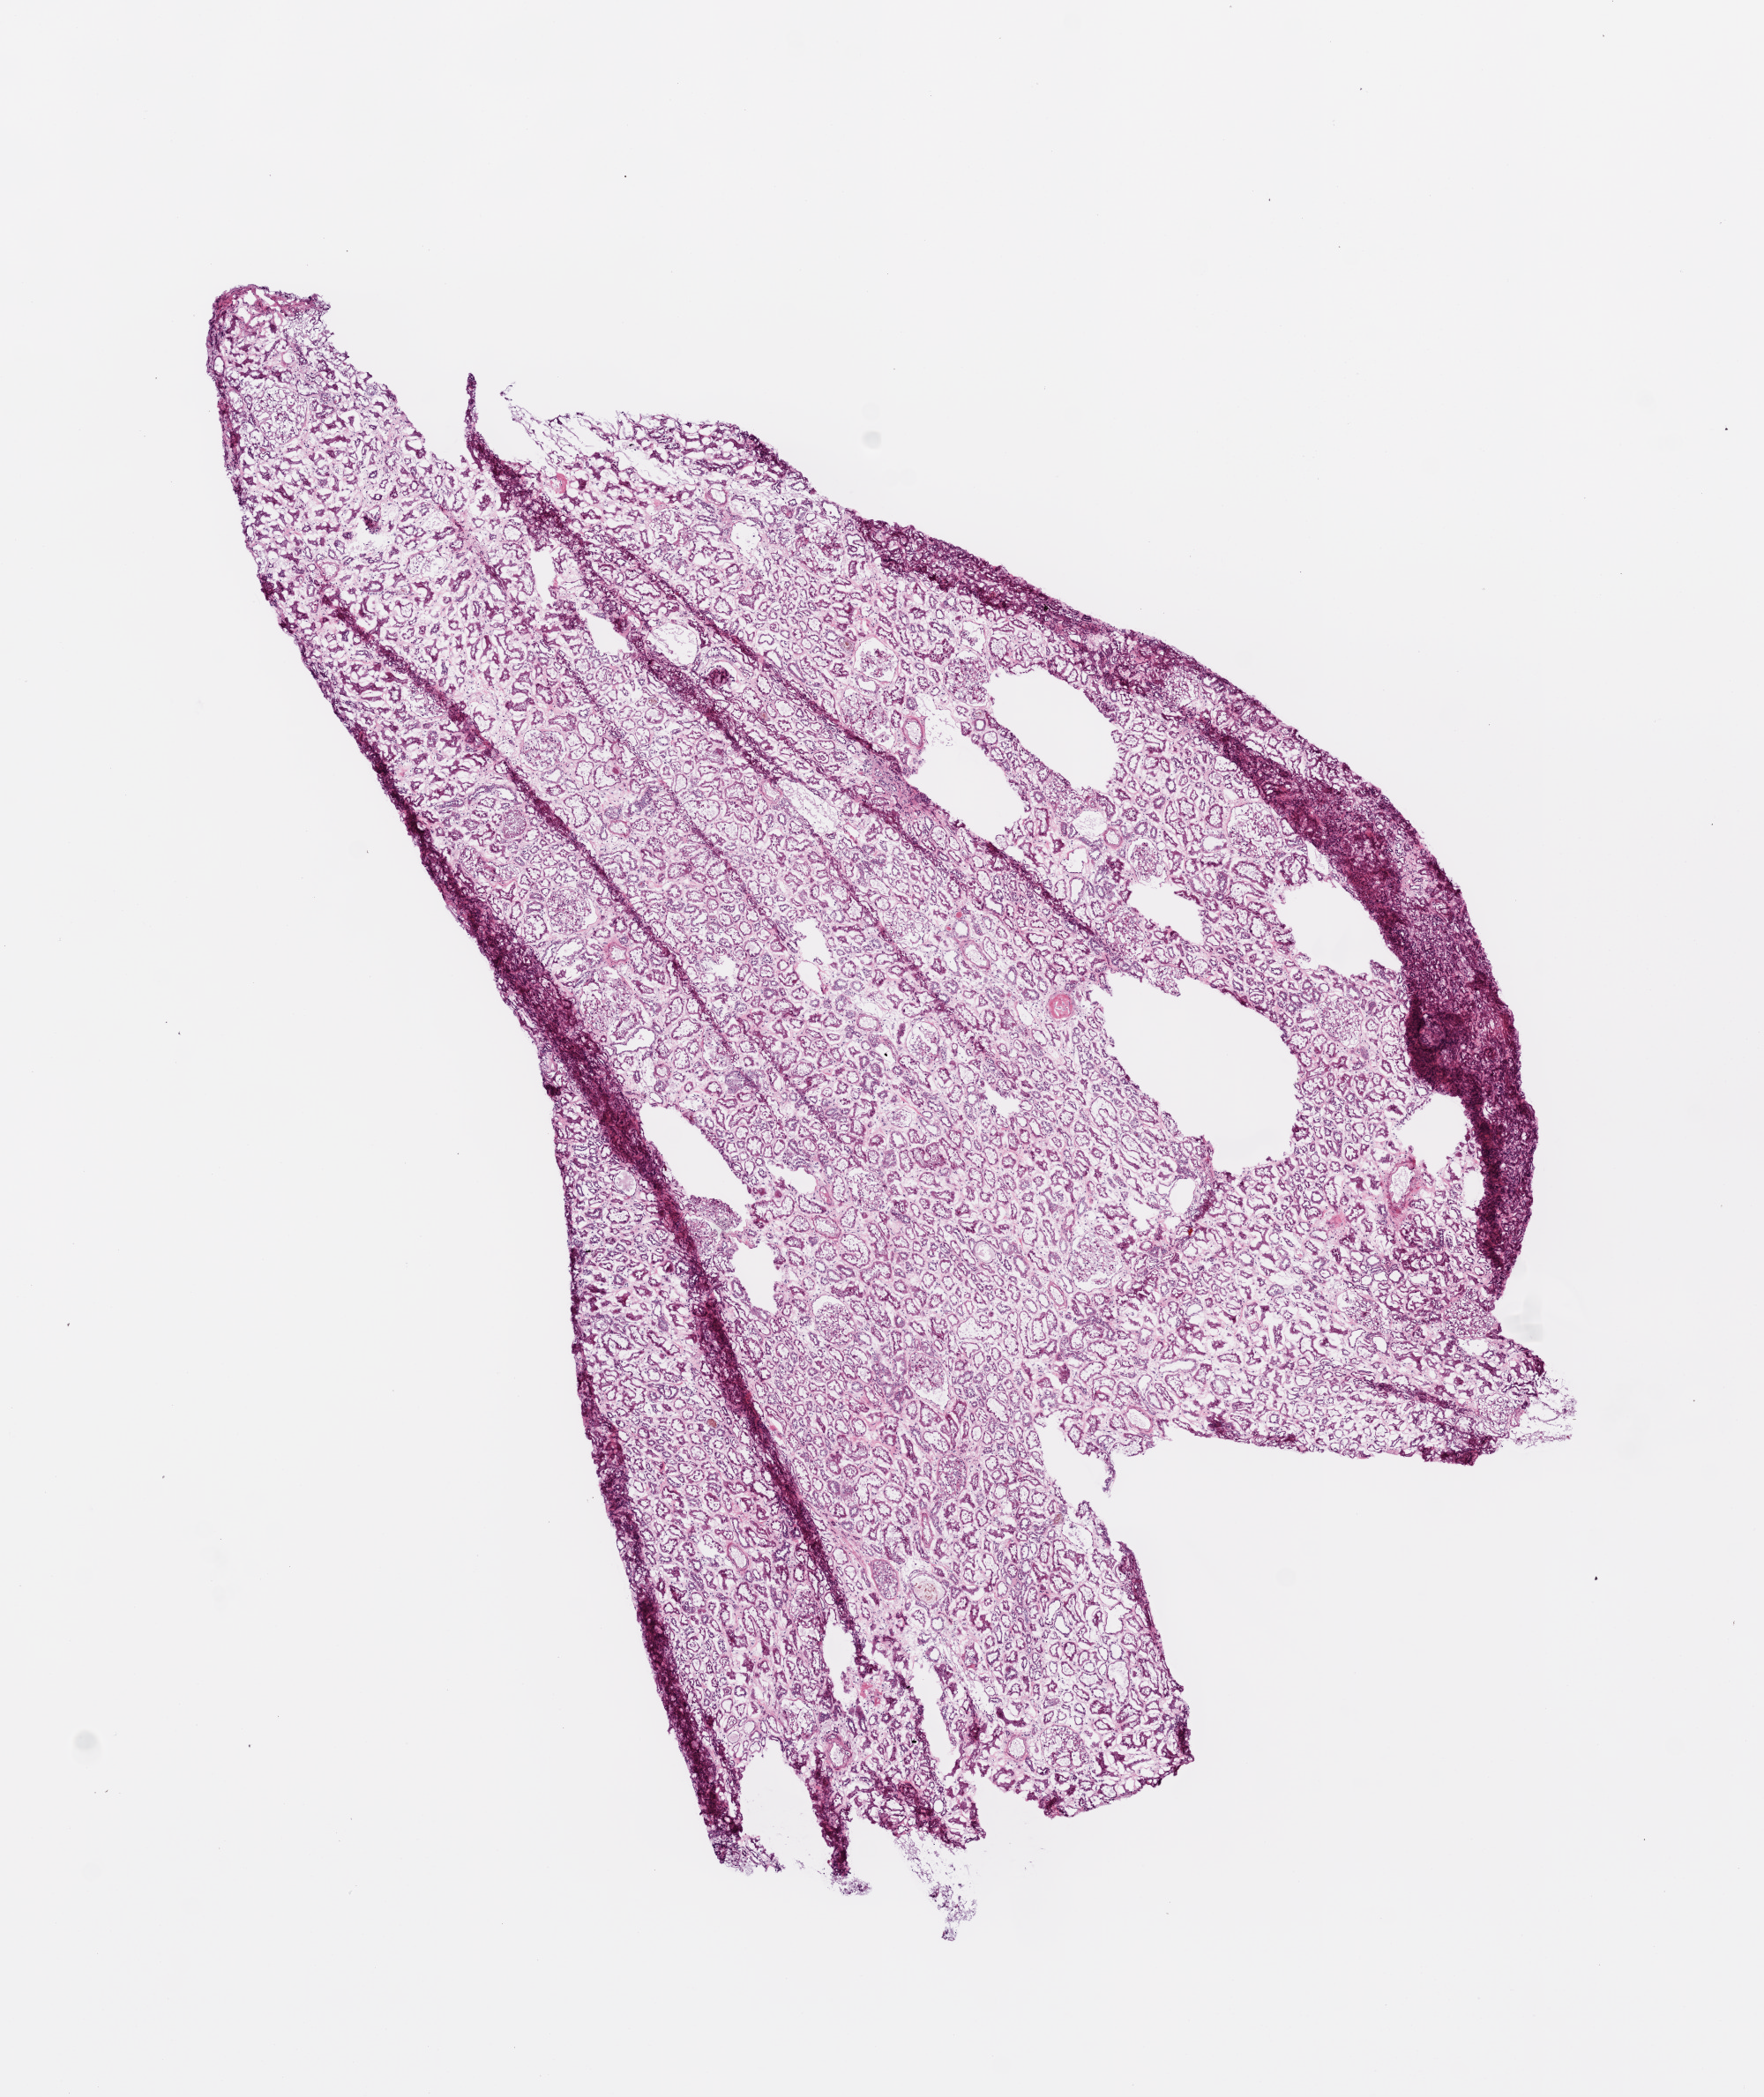
Whole-slide histology image, H&E, a low-resolution overview of the entire scanned area, about 8.0 x 9.5 mm; frozen section from the top of the tissue portion; solid tissue normal (non-tumour tissue) sample from the kidney. Patient: male, age at initial diagnosis 49 years.
This section: solid tissue normal sample (biorepository sample class). Patient diagnosis: Clear cell adenocarcinoma, NOS.